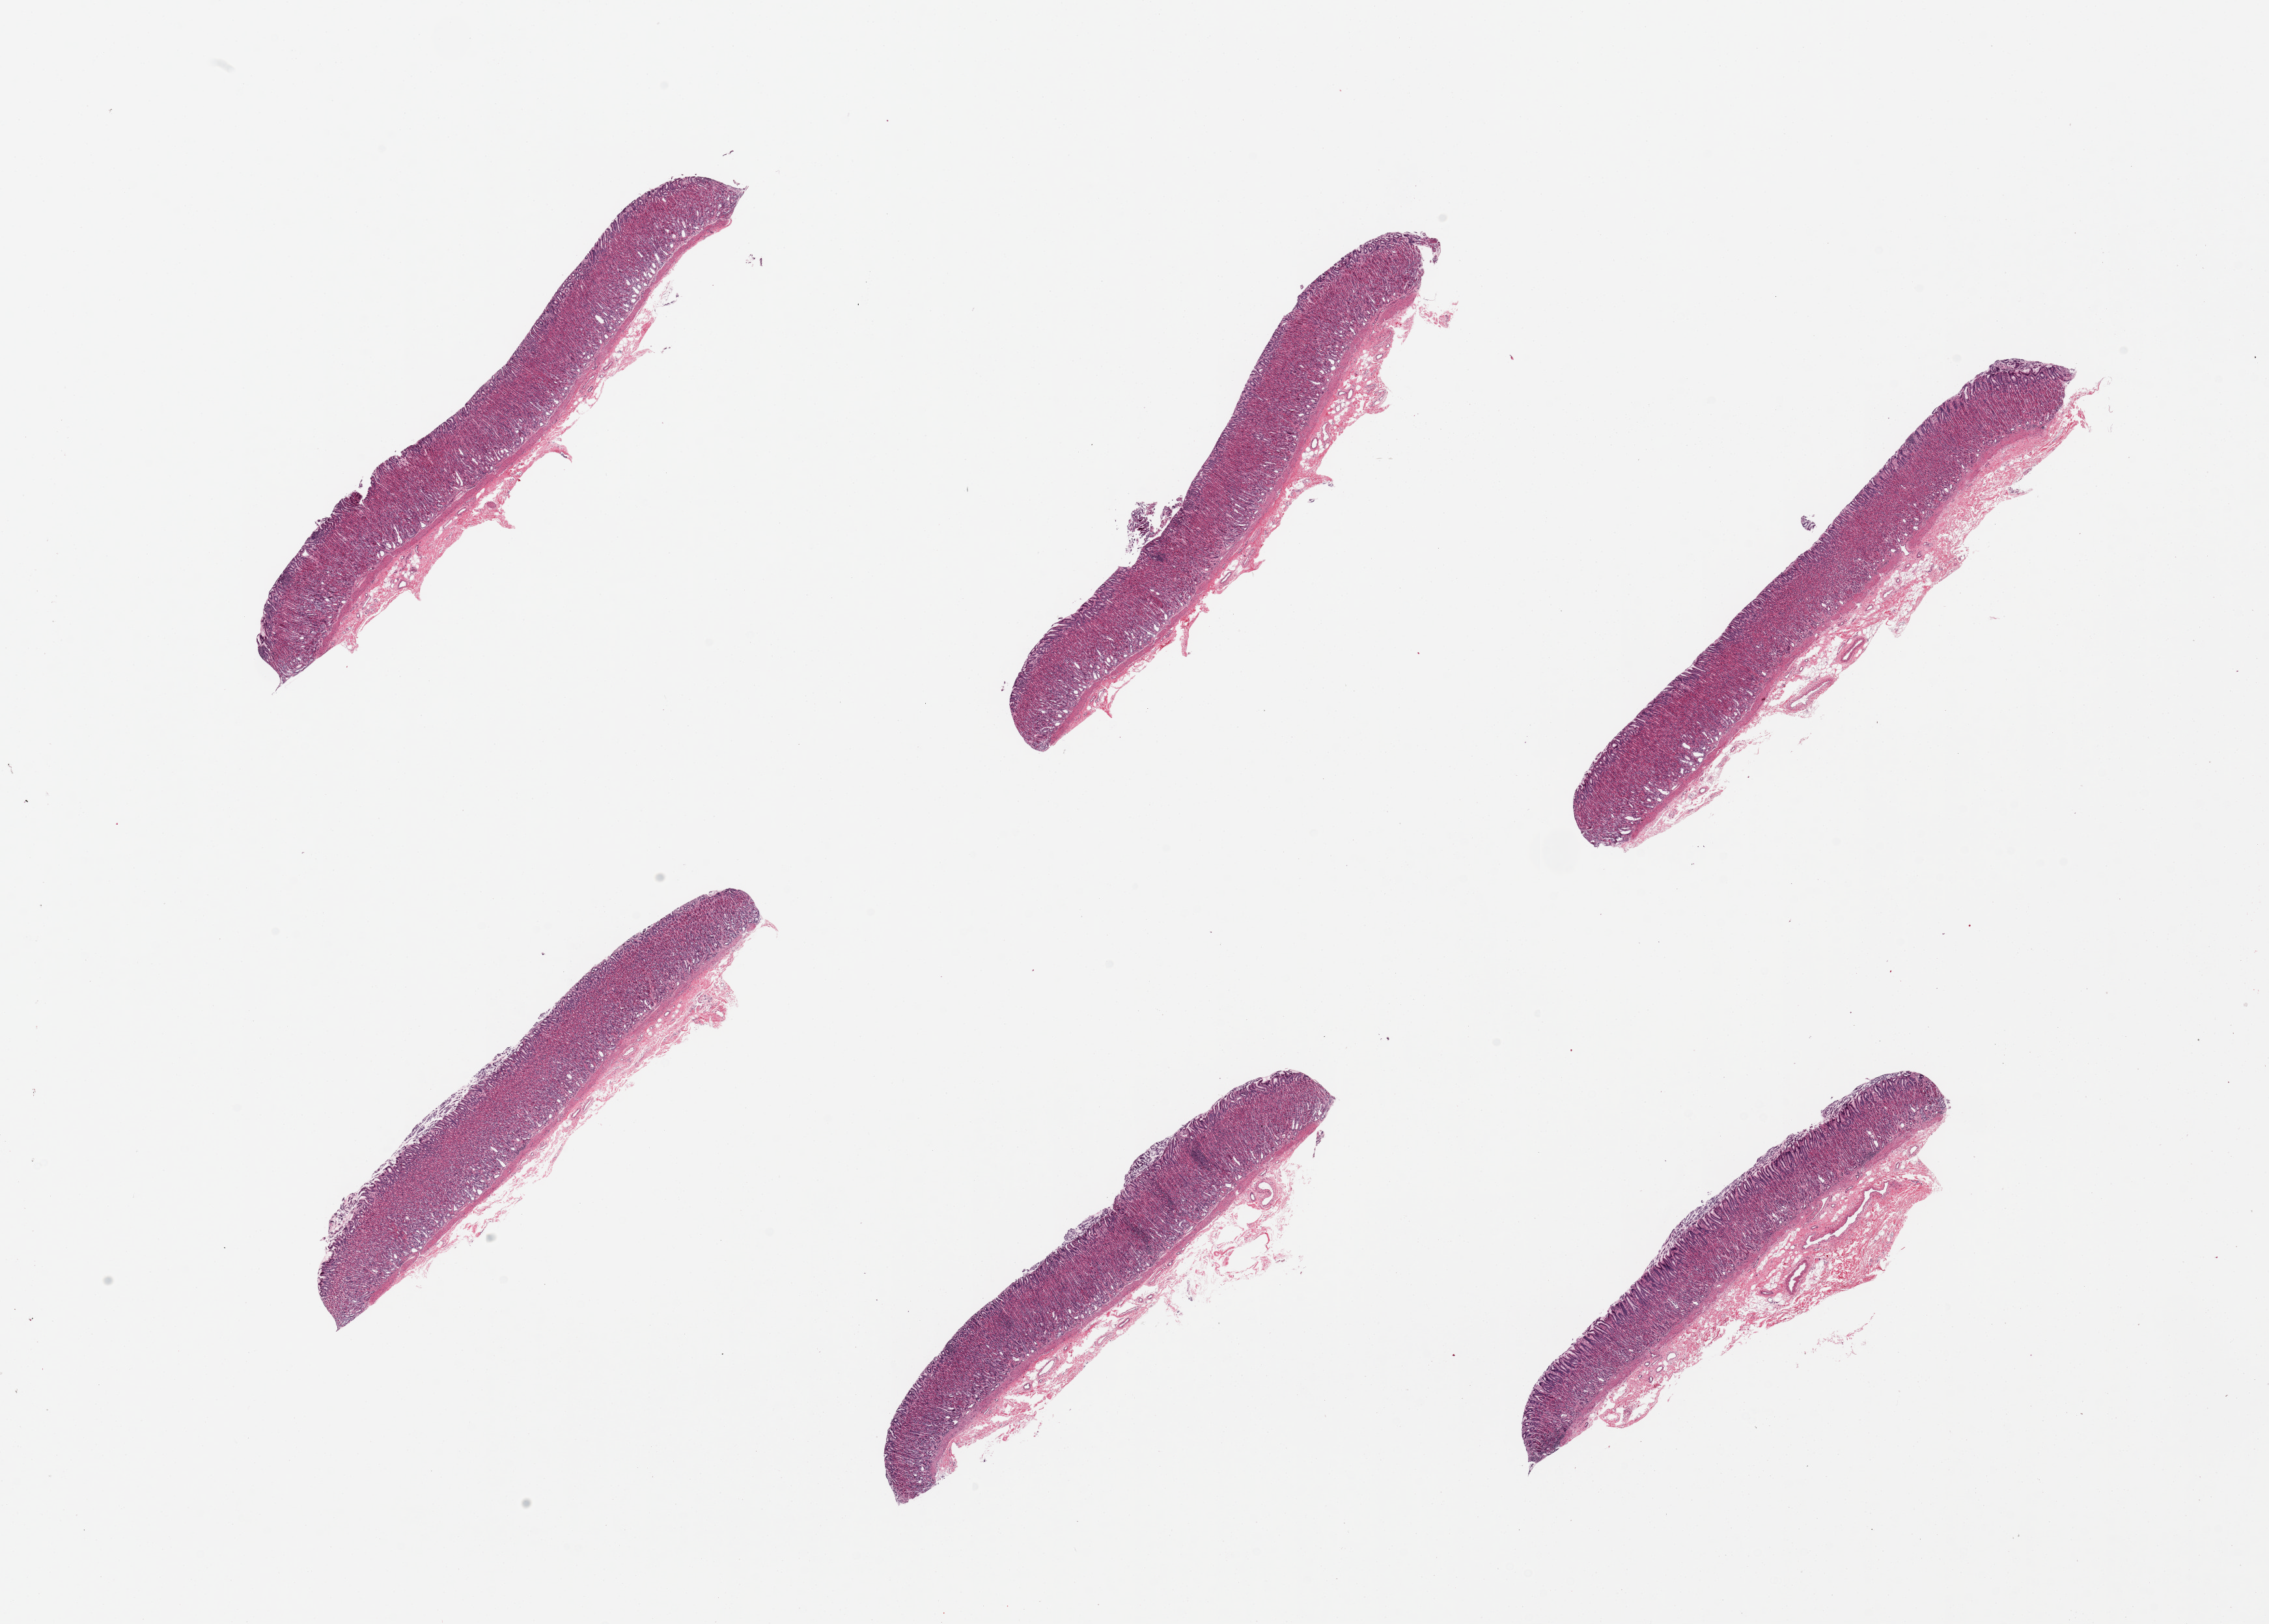
Hematoxylin and eosin (H&E) whole-slide image, low-resolution overview of the scanned area, about 27.6 x 19.7 mm (from a 20x scan). PAXgene-fixed, paraffin-embedded tissue. Sampled site (target tissue): stomach. Tissue donor sample. Donor: female.
- review note (as recorded): 6 pieces, remarkably well-preserved. Mucosa is 60-100% of thickness, excellent specimens